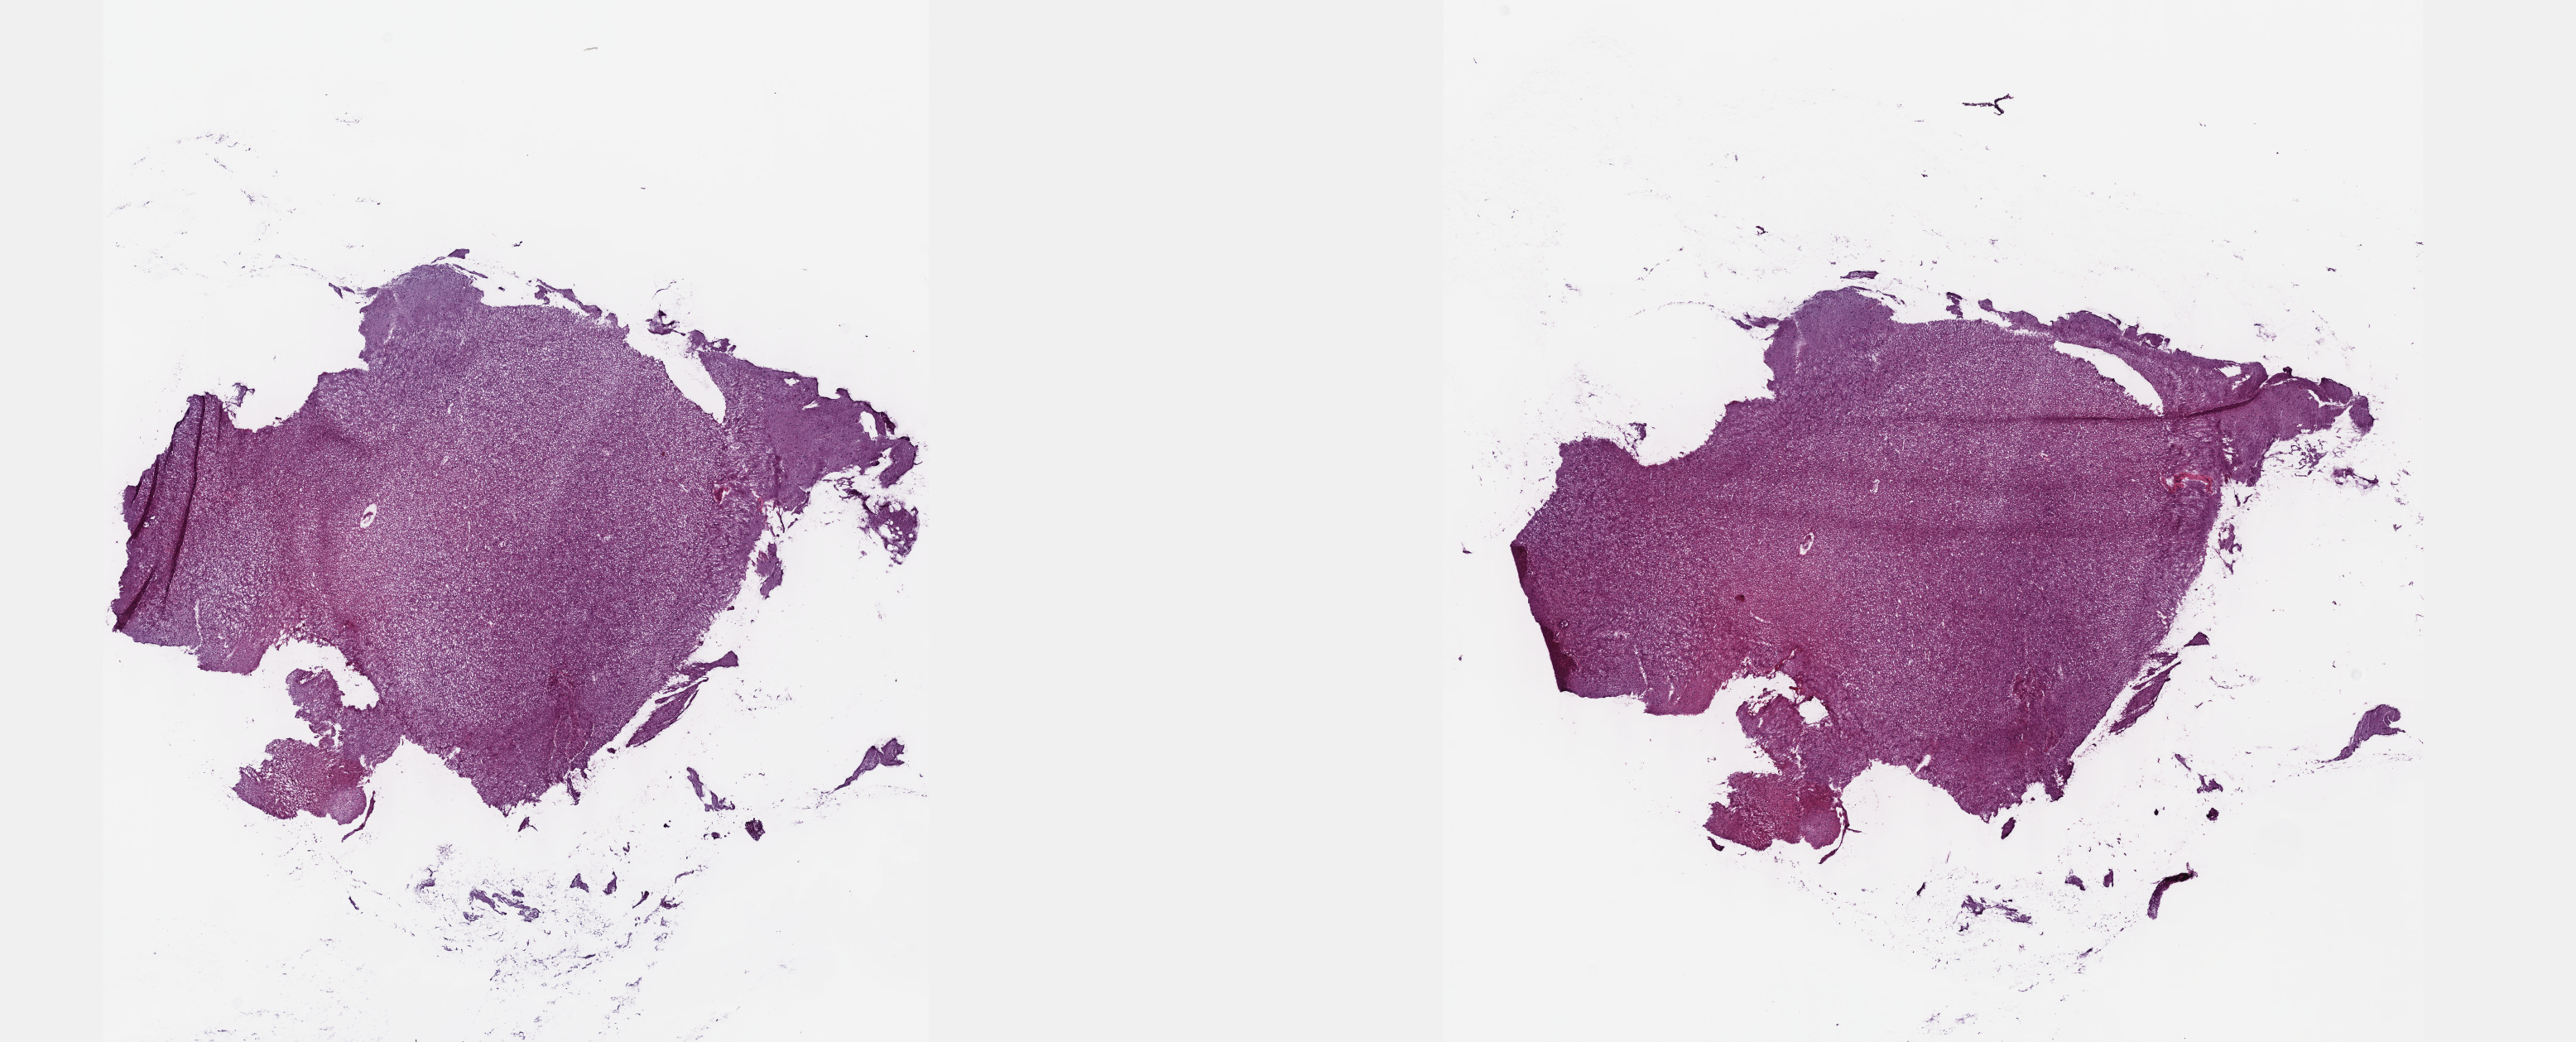
Hematoxylin and eosin (H&E) stained whole-slide image — low-resolution overview of the scanned area, about 25.1 x 10.2 mm (slide scanned at 40x); frozen section; sample: primary tumour, brain. Patient: male, age at initial diagnosis 45 years. Histologic grade: G2 (moderately differentiated). Slide review estimates, as recorded: tumour cells 25%, tumour nuclei 75%, normal cells 10%, stromal cells 65%, necrosis 0%. Infiltration values recorded for this section: lymphocyte infiltration 0%, monocyte infiltration 0%, neutrophil infiltration 0%.
Histologic diagnosis: Oligodendroglioma, NOS (cerebrum). Laterality: right.